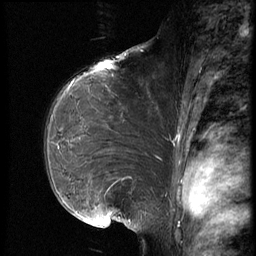
Breast MRI (dynamic contrast-enhanced), one sagittal slice; slice 45 of 66 in the series (ordered by position); dynamic contrast-enhanced series, image 2 of 3 at this slice position (ordered by acquisition); 1.5 T; TE 4.2 ms, TR 8.9 ms; 2.5 mm slice thickness; 256 × 256 image matrix, field of view 200 × 200 mm. Patient: female, 39 years. Case-level facts recorded for this patient, not image findings: setting: breast cancer imaged before/during neoadjuvant chemotherapy; receptor status: HER2-positive.
Annotated regions visible in this slice (semi-automatic segmentation, software-assisted and operator-edited):
- analysis volume of interest (the breast-tissue region the enhancement analysis was run in; not a lesion): bounding box (x1, y1, x2, y2) in pixels: (42, 75, 172, 218)
- tumour enhancement mask (voxels above the 140 % enhancement threshold inside the analysis volume of interest): (108, 179, 123, 181)